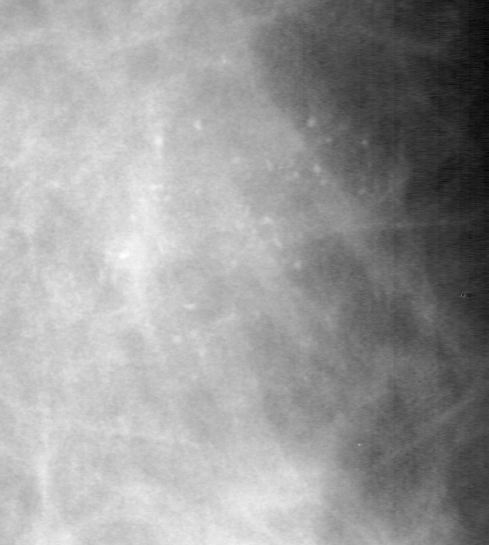
Region of interest cut from a scanned film mammogram (one marked finding); right breast; MLO view.
- Calcifications, morphology pleomorphic, distribution clustered; BI-RADS assessment category 4; pathology (as recorded): malignant.